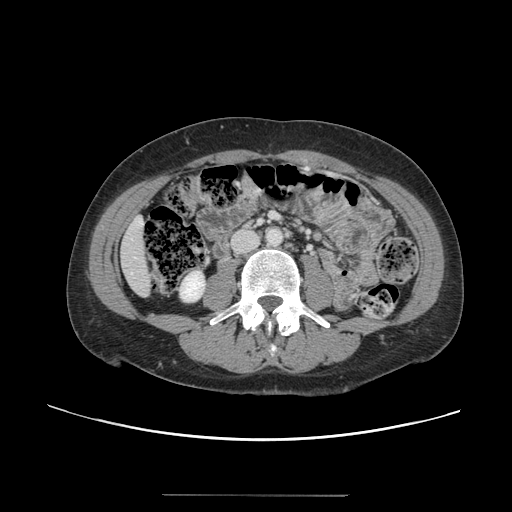
Contrast-enhanced abdominal CT, one axial slice. Intravenous contrast given. Soft-tissue window (W 400 / L 40 HU). 2.5 mm slice thickness. 512 × 512 image matrix, field of view 380 × 380 mm. Female patient, age 53 years. Case-level facts recorded for this patient, not image findings: diagnosis: colorectal cancer liver metastases, imaged before liver resection; multiple liver metastases: yes; largest metastasis: 1.1 cm; chemotherapy before resection: no.
Annotated regions visible in this slice (manually delineated by an expert):
- liver: bounding box <120,216,151,296> (left, top, right, bottom; pixels)
- planned liver remnant (the part of the liver to remain after resection): <120,217,151,297>